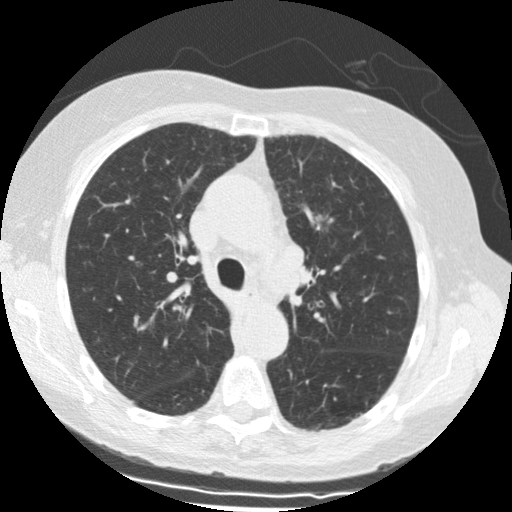
Axial slice from a low-dose chest CT screening exam. Baseline annual screen. Lung window (W 1500 / L -600 HU). 2.5 mm slice thickness. Standard (soft-tissue) reconstruction kernel (STANDARD). Slice 43 of 139 in the series. Female participant, aged 69 years at enrolment. Former smoker at enrolment.
- Expert-annotated lung lesion, box from (x=298, y=205) to (x=344, y=245) px.
- The screening reader recorded 2 non-calcified nodules or masses ≥4 mm on this exam (left upper lobe, left upper lobe); which of them this box marks is not recorded.
- Later outcome: lung cancer diagnosed 18 days after this screen — squamous cell carcinoma, NOS, left upper lobe, stage IIIA (AJCC 6th edition), 15 mm at pathology.